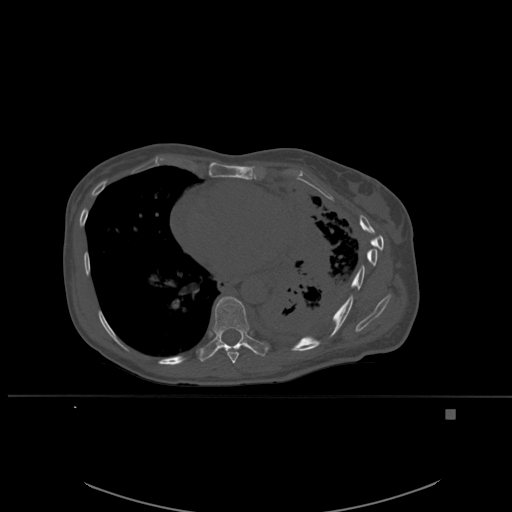
CT including the spine, one axial slice; slice 339 of 537 in the series (ordered by position); bone window (W 1800 / L 400 HU); 1.5 mm slice thickness; 512 × 512 image matrix, field of view 440 × 440 mm. Patient: female, 45 years. Case-level facts recorded for this patient, not image findings: primary cancer: lung.
Structures marked on this image (semi-automatic segmentation, software-assisted and operator-edited):
- T8 vertebra: box from (x=226, y=347) to (x=239, y=364) px
- T9 vertebra: (x=198, y=296)–(x=269, y=362)